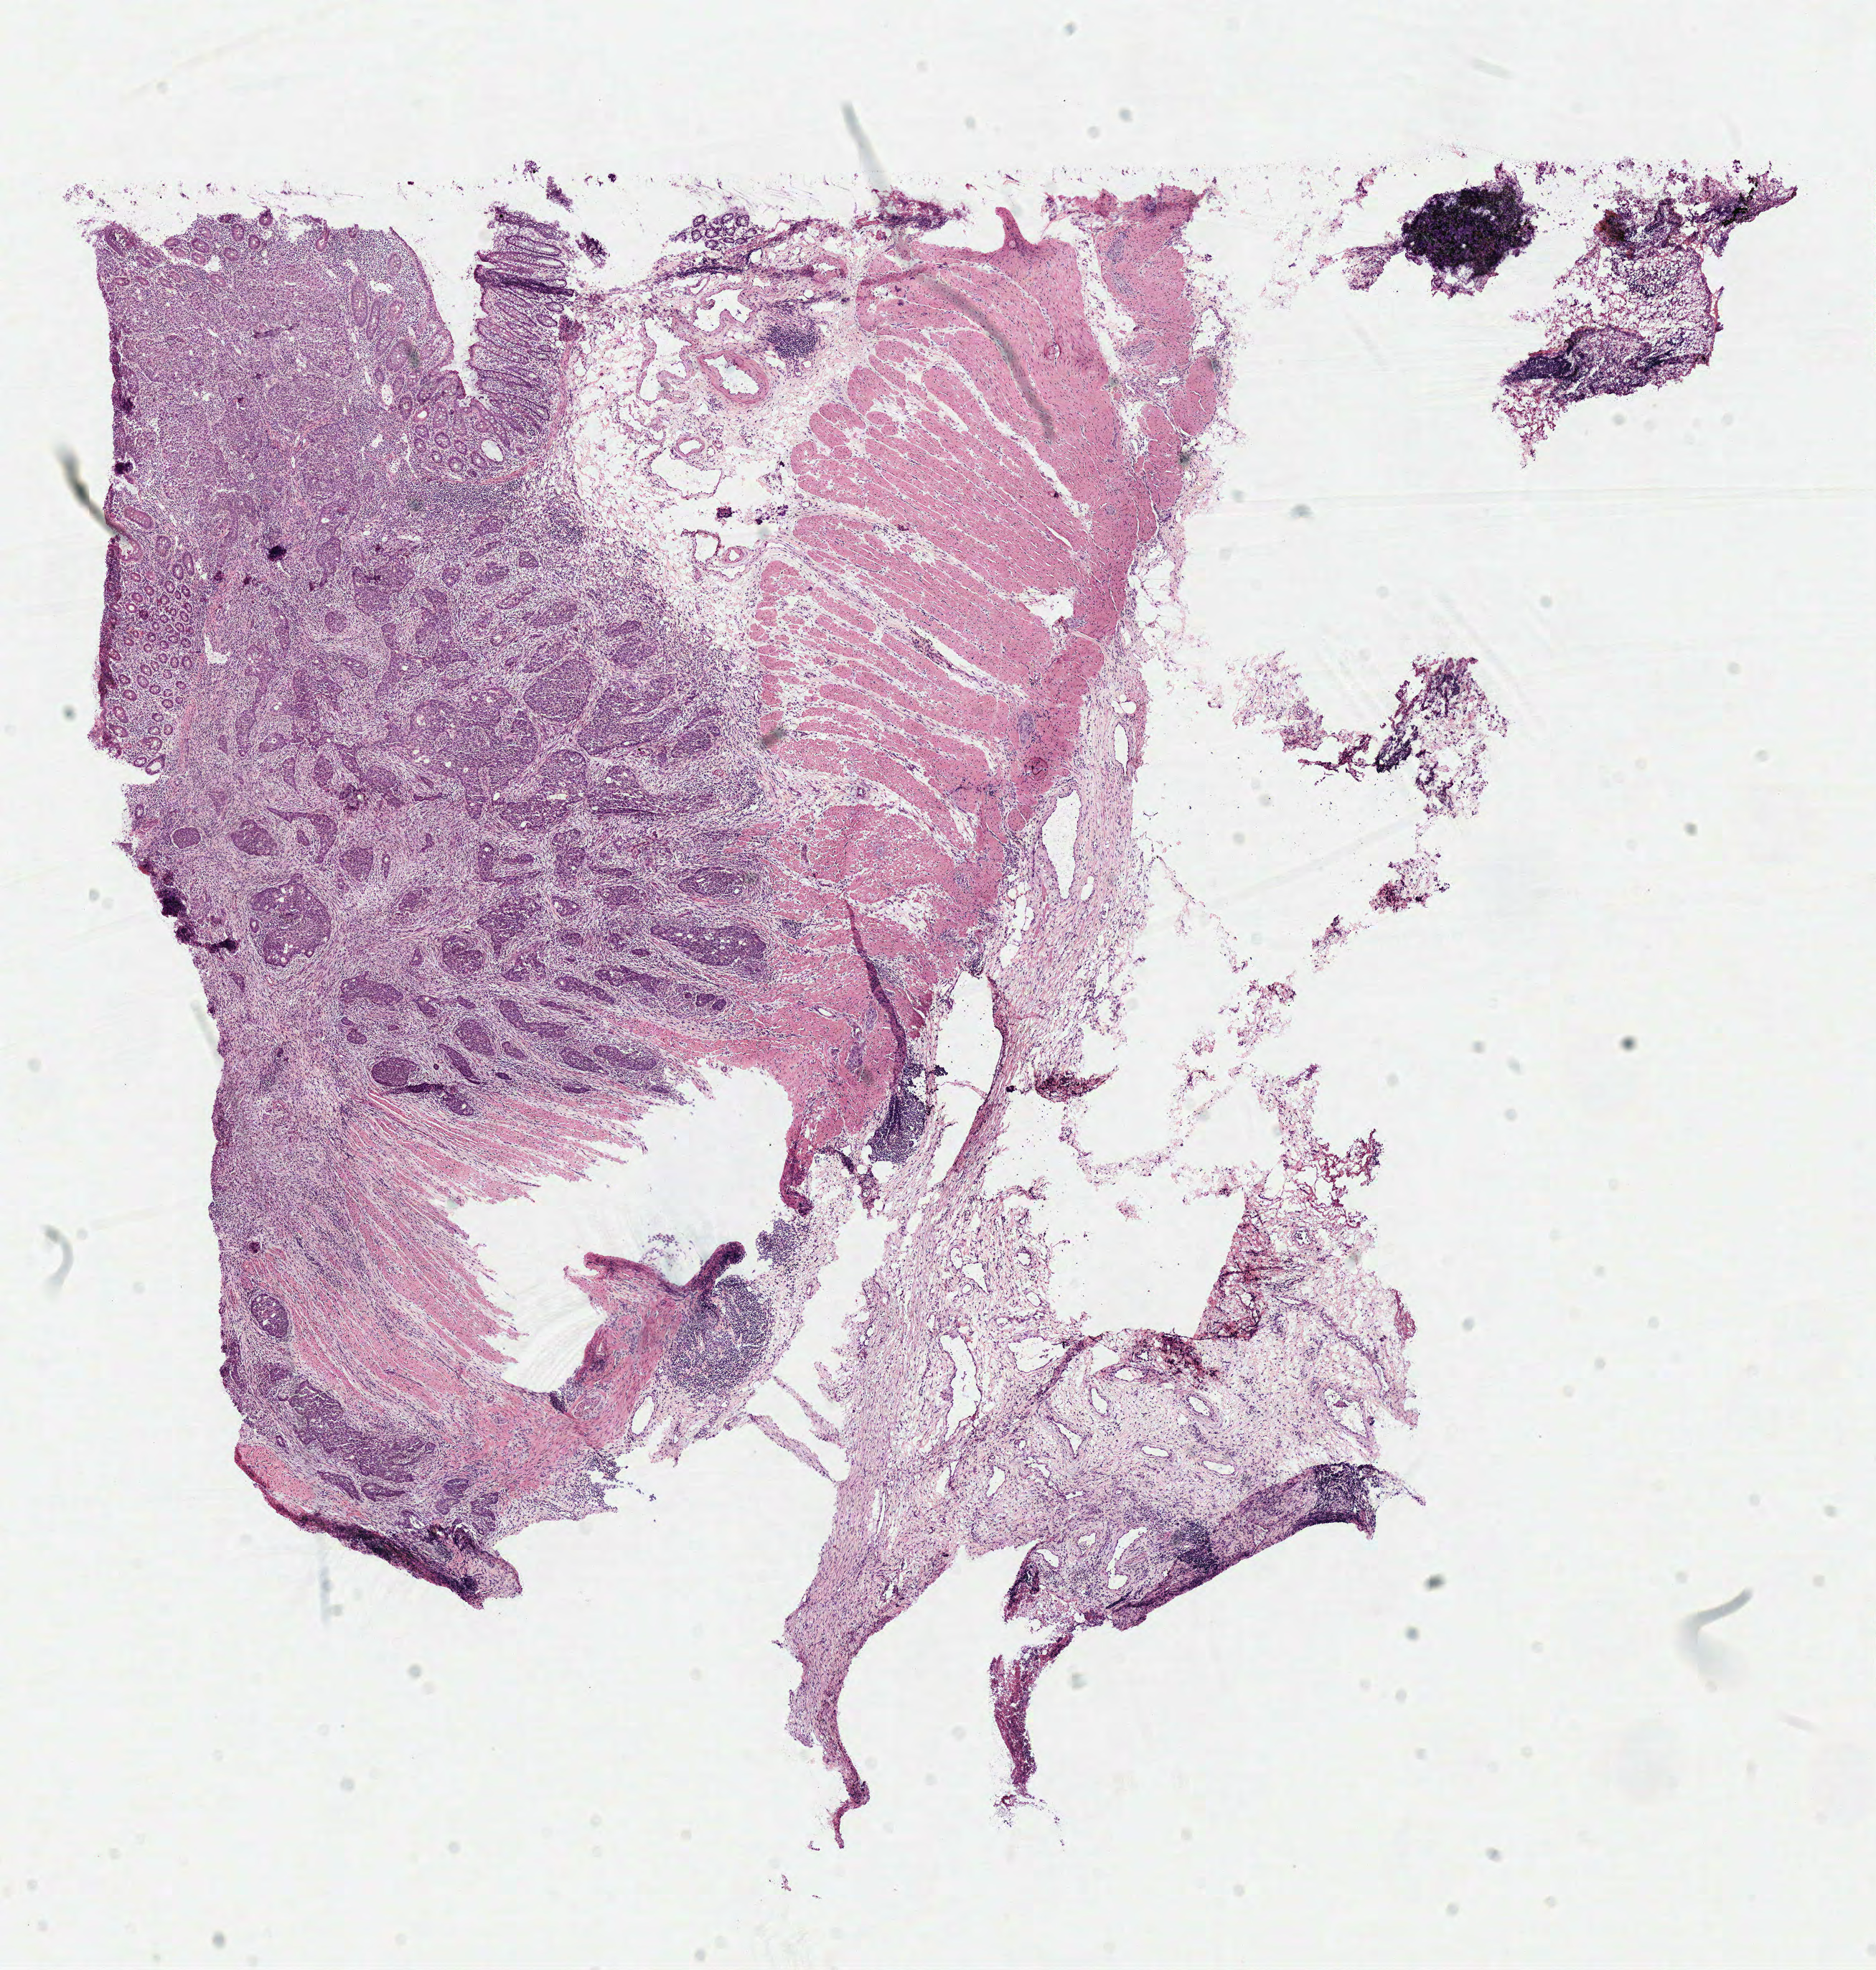
Digitized Hematoxylin and eosin (H&E) stained tissue section (whole slide), shown as a low-resolution overview of the whole scanned area (about 10.3 x 10.8 mm, acquisition: 40x scan). Frozen section. Primary tumour sample from the colon. Female, age 66 years at initial diagnosis. Slide review estimates, as recorded: tumour cells 54%, tumour nuclei 65%, normal cells 5%, stromal cells 40%, necrosis 1%.
AJCC pathologic stage: IIB (6th edition). Pathologic diagnosis: Adenocarcinoma, NOS (transverse colon).